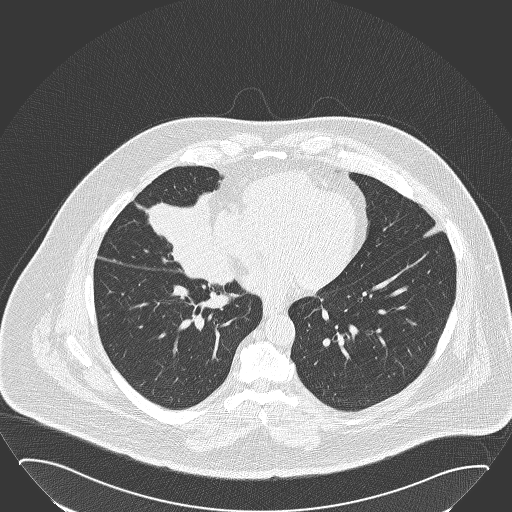
Axial slice from a low-dose chest CT screening exam, baseline annual screen, lung window (W 1500 / L -600 HU), 2 mm slice thickness, lung (sharp) reconstruction kernel (B50f), 120 kVp, 512 × 512 image matrix, field of view 432 × 432 mm. Male, age 61 years at enrolment. Former smoker at enrolment.
Expert-annotated lung lesion, box from (x=138, y=183) to (x=229, y=271) px. The screening reader recorded 2 non-calcified nodules or masses ≥4 mm on this exam (right middle lobe, left lower lobe); which of them this box marks is not recorded. Participant outcome: lung cancer diagnosed 47 days after this screen — basaloid squamous cell carcinoma, right middle lobe, right hilum, poorly differentiated (G3), stage IIB (AJCC 6th edition), 95 mm at pathology.